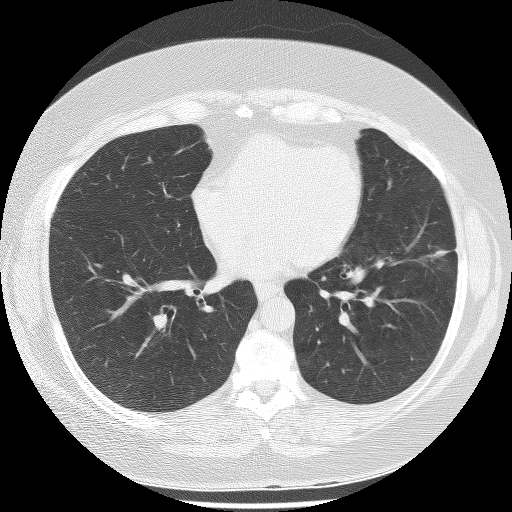
Low-dose screening chest CT, one axial slice; position 109 of 233 along the scan axis; reconstruction kernel BONE; lung window (W 1500 / L -600 HU); 2.5 mm slice thickness; 512 × 512 image matrix.
Annotated regions visible in this slice (manually delineated by an expert):
- lesion 1 (tumor, lower lobe of left lung): bounding box <427,250,457,261> (left, top, right, bottom; pixels)